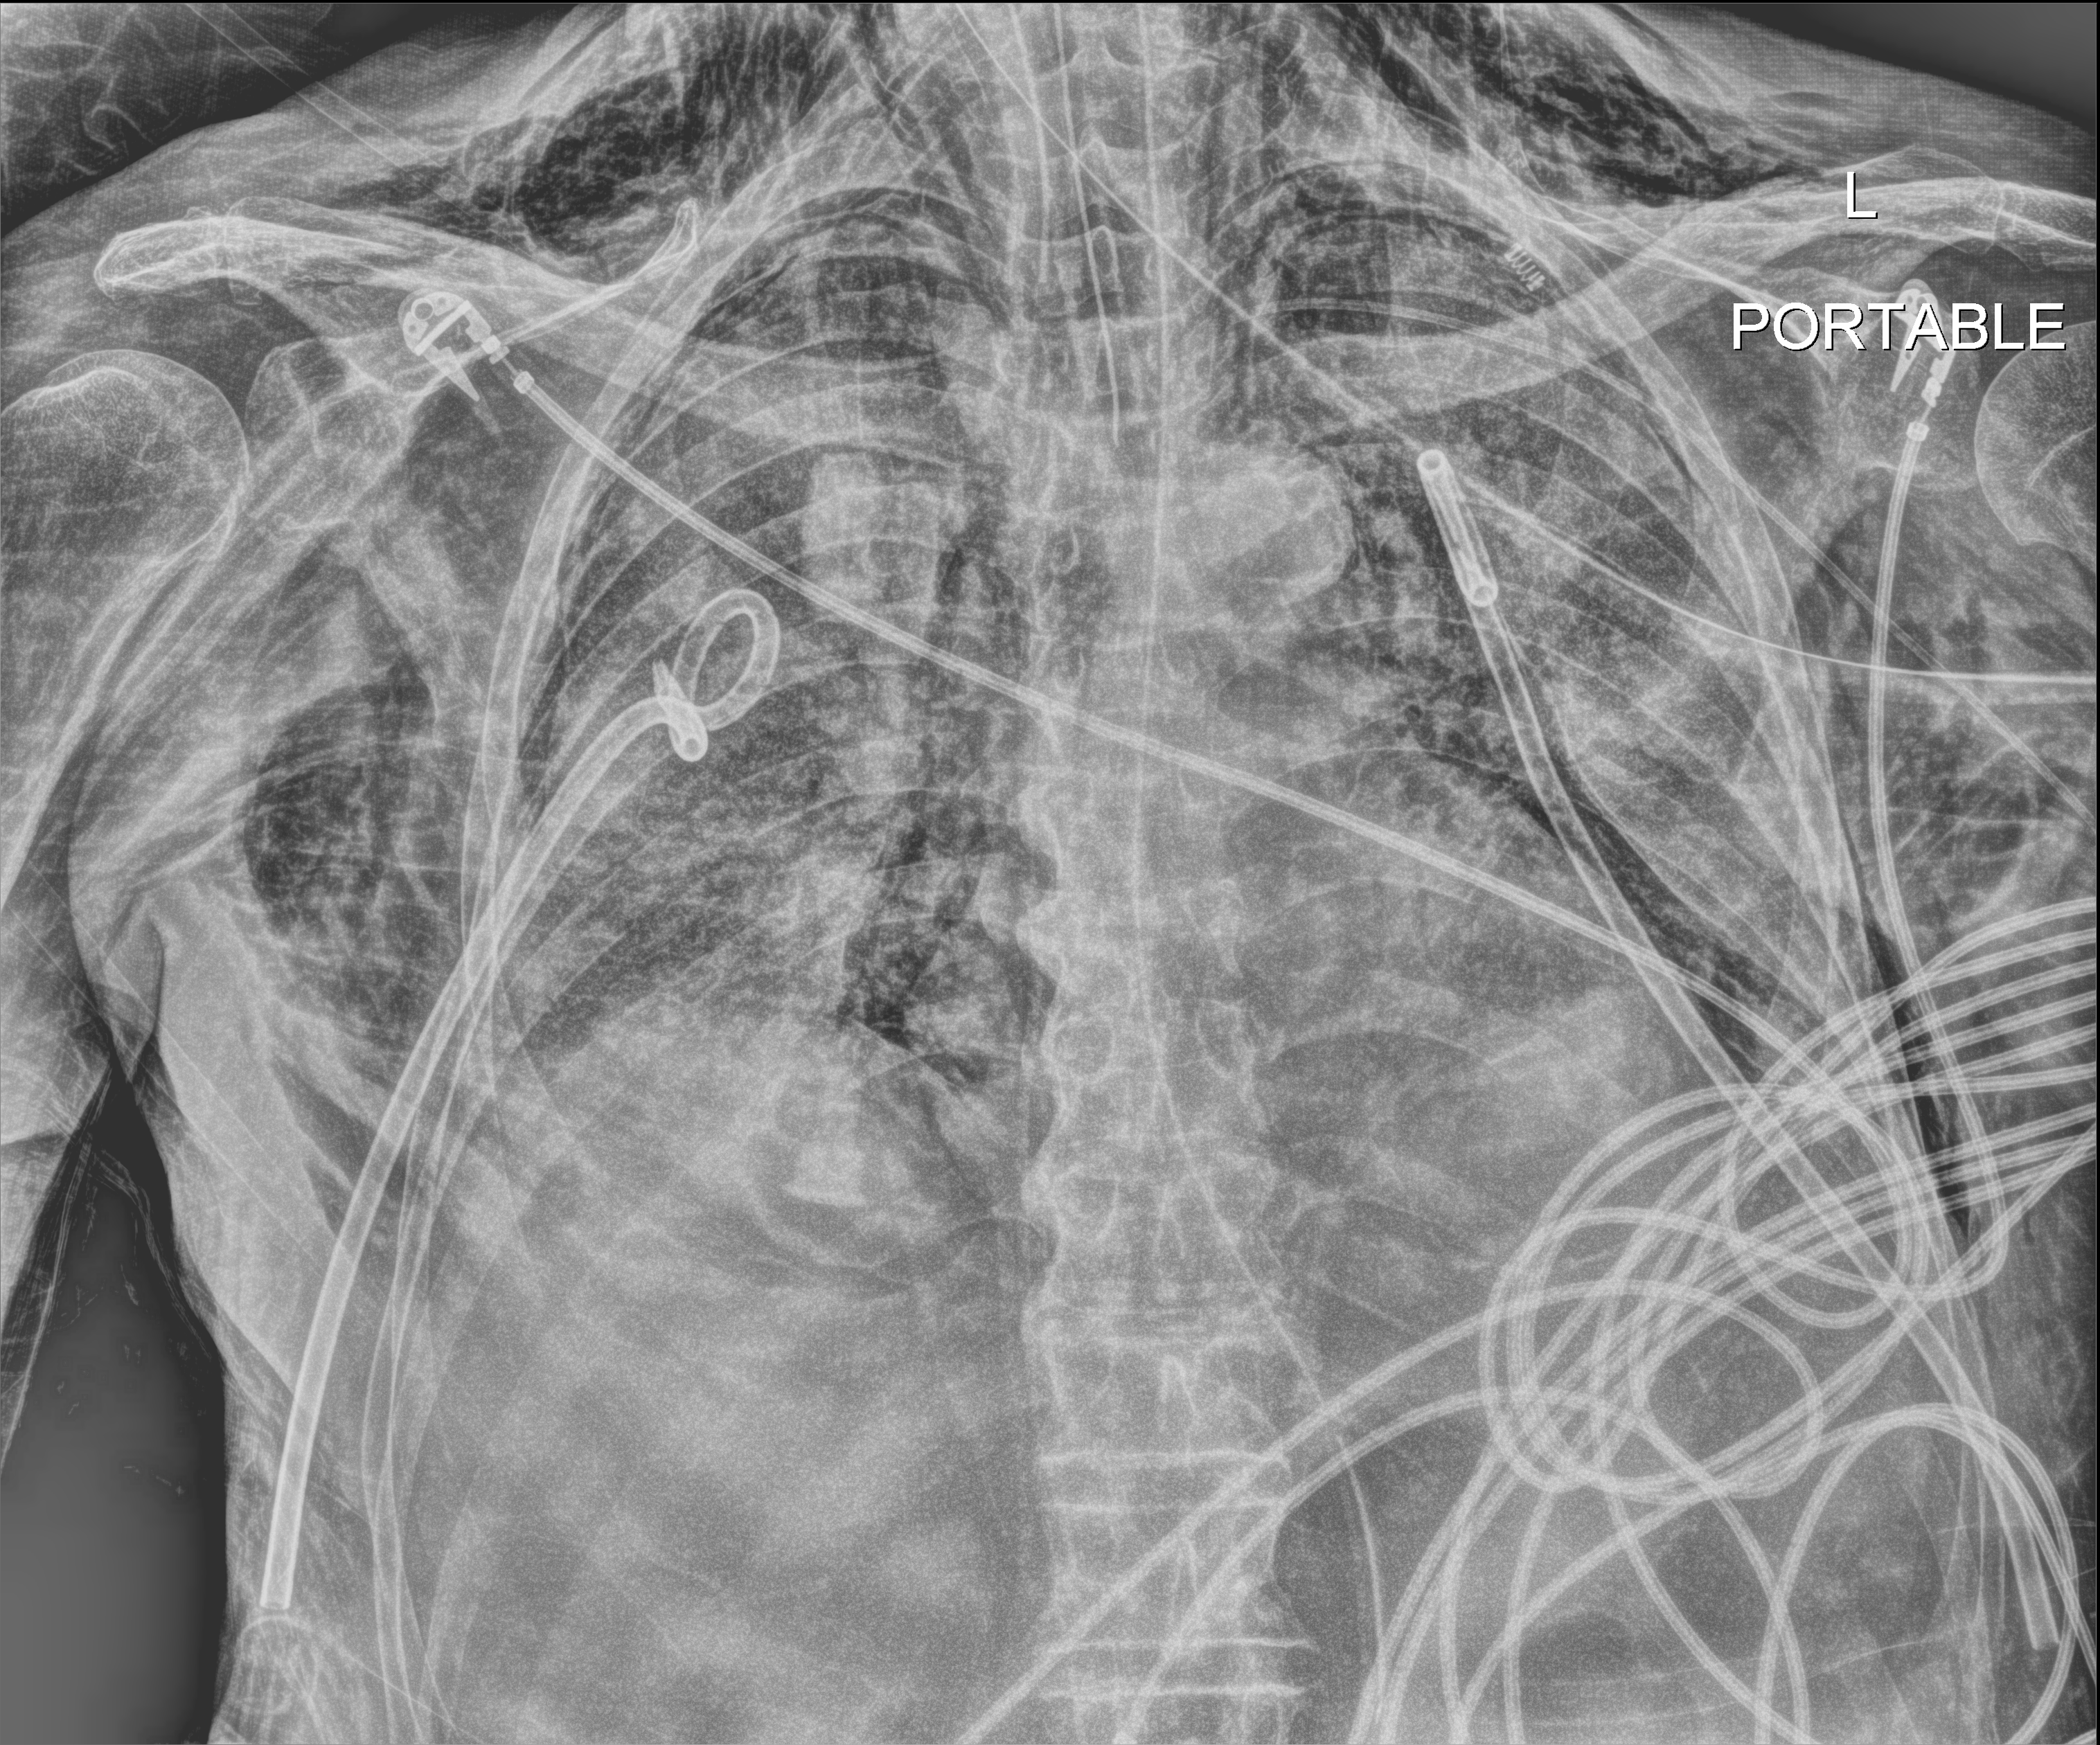
Chest X-ray (portable); anteroposterior (AP) projection. Male patient hospitalised with COVID-19, age 75–90 years.
From the hospital-stay record, not from the radiograph (when in the stay this image was taken is not recorded): chronic kidney disease (admission record): no; mechanically ventilated during this hospital stay: yes; admitted to intensive care during this hospital stay: yes.